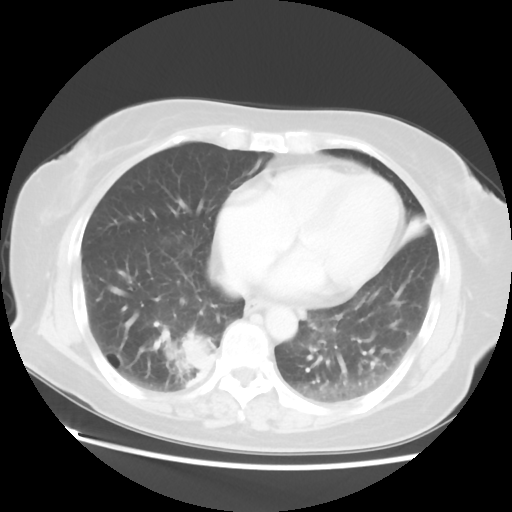
Chest CT, one axial slice. Slice 21 of 52 in the series (ordered by position). Lung window (W 1500 / L -600 HU). 5 mm slice thickness. 512 × 512 image matrix, field of view 356 × 356 mm. Female patient, age 69 years. From the clinical record (not read from this slice): clinical TNM (as recorded): T2 N1 M1a.
Outlined on this slice (bounding box drawn by a radiologist):
- lung tumour (recorded histology: adenocarcinoma): box from (x=172, y=331) to (x=213, y=390) px